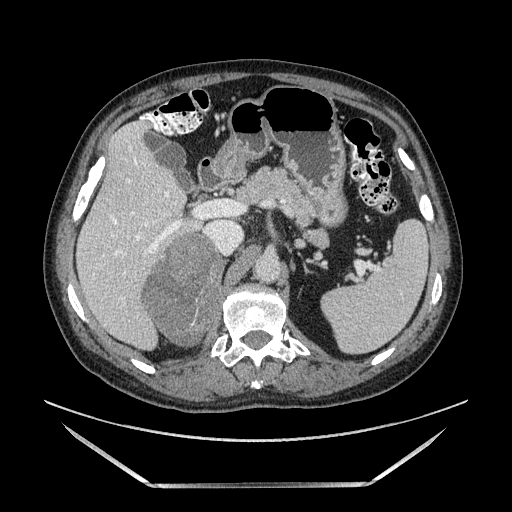
Contrast-enhanced abdominal CT, one axial slice. Slice 90 of 185 in the series (ordered by position). Soft-tissue window (W 400 / L 40 HU). 1.25 mm slice thickness. 512 × 512 image matrix, field of view 440 × 440 mm. Male patient. Case-level facts recorded for this patient, not image findings: diagnosis: adrenocortical carcinoma; tumour side: right adrenal; tumour size at pathology: 10.3 cm; Ki-67 index: 20 %.
Annotated regions visible in this slice (semi-automatic segmentation, software-assisted and operator-edited):
- mass: box from (x=147, y=235) to (x=227, y=346) px